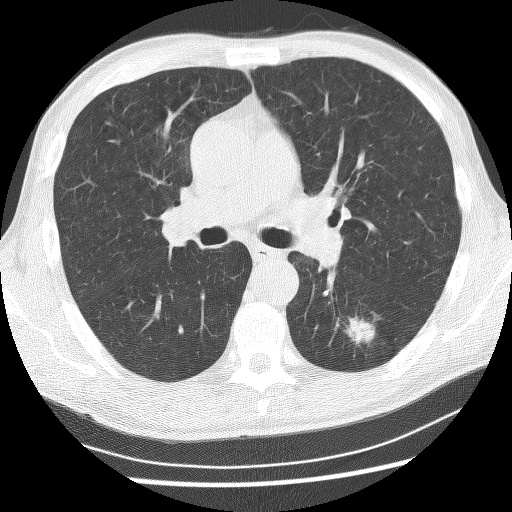
Chest CT (low-dose screening protocol), one axial image; baseline screening round; lung window (W 1500 / L -600 HU); 2.5 mm slice thickness; lung (sharp) reconstruction kernel (BONE); slice 104 of 253 in the series. Male participant, aged 62 years at enrolment. Current smoker at enrolment.
- Expert-annotated lung lesion, bounding box [x1, y1, x2, y2] px = [331, 309, 381, 355].
- Screening reader's record for this exam (one nodule recorded; not confirmed to be the boxed lesion): non-calcified nodule or mass ≥4 mm, left lower lobe, 21 × 17 mm, spiculated (stellate) margins, soft tissue attenuation.
- Official screen result: positive, change unspecified: nodule(s) >= 4 mm or enlarging nodule(s), mass(es), or other non-specific abnormalities suspicious for lung cancer.
- Later outcome: lung cancer diagnosed 58 days after this screen — non-small cell carcinoma, left lower lobe, poorly differentiated (G3), stage IA (AJCC 6th edition), 11 mm at pathology.